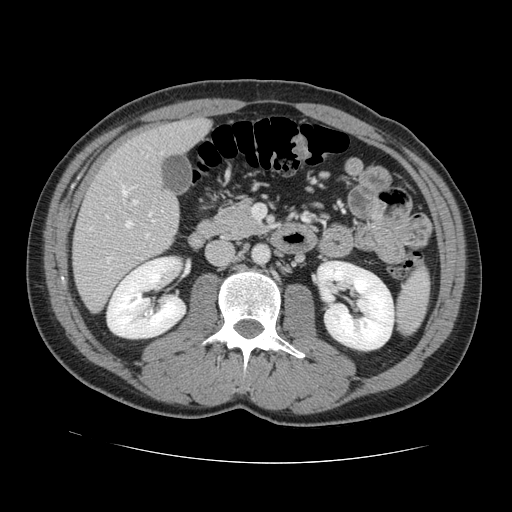
Contrast-enhanced abdominal CT, one axial slice. Slice 54 of 131 in the series (ordered by position). 120 kVp. Intravenous contrast given. Soft-tissue window (W 400 / L 40 HU). 2.5 mm slice thickness. 512 × 512 image matrix, field of view 380 × 380 mm. Male patient, age 40 years. Case-level facts recorded for this patient, not image findings: diagnosis: colorectal cancer liver metastases, imaged before liver resection; multiple liver metastases: yes; largest metastasis: 2.9 cm.
Annotated regions visible in this slice (outlined manually by an expert reader):
- hepatic veins: bounding box [x1, y1, x2, y2] px = [106, 152, 163, 262]
- liver: [74, 119, 209, 310]
- planned liver remnant (the part of the liver to remain after resection): [116, 120, 210, 172]
- portal vein (with intrahepatic branches): [132, 200, 150, 238]